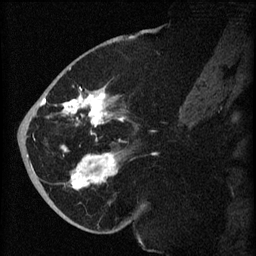
Breast MRI (dynamic contrast-enhanced), one sagittal slice. Dynamic contrast-enhanced series, image 2 of 3 at this slice position (ordered by acquisition). 1.5 T. TE 4.2 ms, TR 8.2 ms. 2 mm slice thickness. 256 × 256 image matrix. Patient: female, 71 years.
Outlined on this slice (semi-automatically segmented with operator editing):
- analysis volume of interest (the breast-tissue region the enhancement analysis was run in; not a lesion): bounding box [x1, y1, x2, y2] px = [40, 72, 139, 196]
- tumour enhancement mask (voxels above the 70 % enhancement threshold inside the analysis volume of interest): [40, 87, 124, 190]